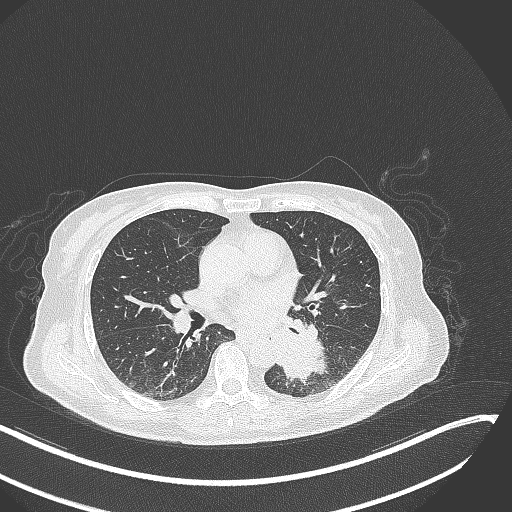
Chest CT, one axial slice. Slice 139 of 342 in the series (ordered by position). Reconstruction kernel B70f. 120 kVp. Lung window (W 1500 / L -600 HU). 1 mm slice thickness. 512 × 512 image matrix, field of view 400 × 400 mm. Female patient, age 64 years. From the clinical record (not read from this slice): clinical TNM (as recorded): T3 N1 M1; histopathological grade: G3.
Annotated regions visible in this slice (bounding box drawn by a radiologist):
- lung tumour (recorded histology: small cell carcinoma): bounding box <269,327,334,383> (left, top, right, bottom; pixels)